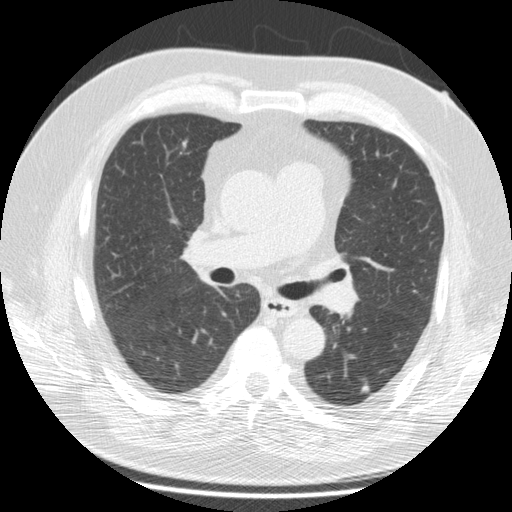
Low-dose screening chest CT, axial slice; third screening round (two years after baseline); lung window (W 1500 / L -600 HU); slice 71 of 172 in the series; 512 × 512 image matrix. Male, age 69 years at enrolment. Former smoker at enrolment.
Expert reader's lesion annotation, box from (x=353, y=372) to (x=381, y=401) px. The screening reader recorded 2 non-calcified nodules or masses ≥4 mm on this exam (left lower lobe, left lower lobe); which of them this box marks is not recorded. Official screen result: positive, other. Participant outcome: lung cancer diagnosed 224 days after this screen — squamous cell carcinoma, NOS, left lower lobe, moderately differentiated (G2), stage IA (AJCC 6th edition), 14 mm at pathology.